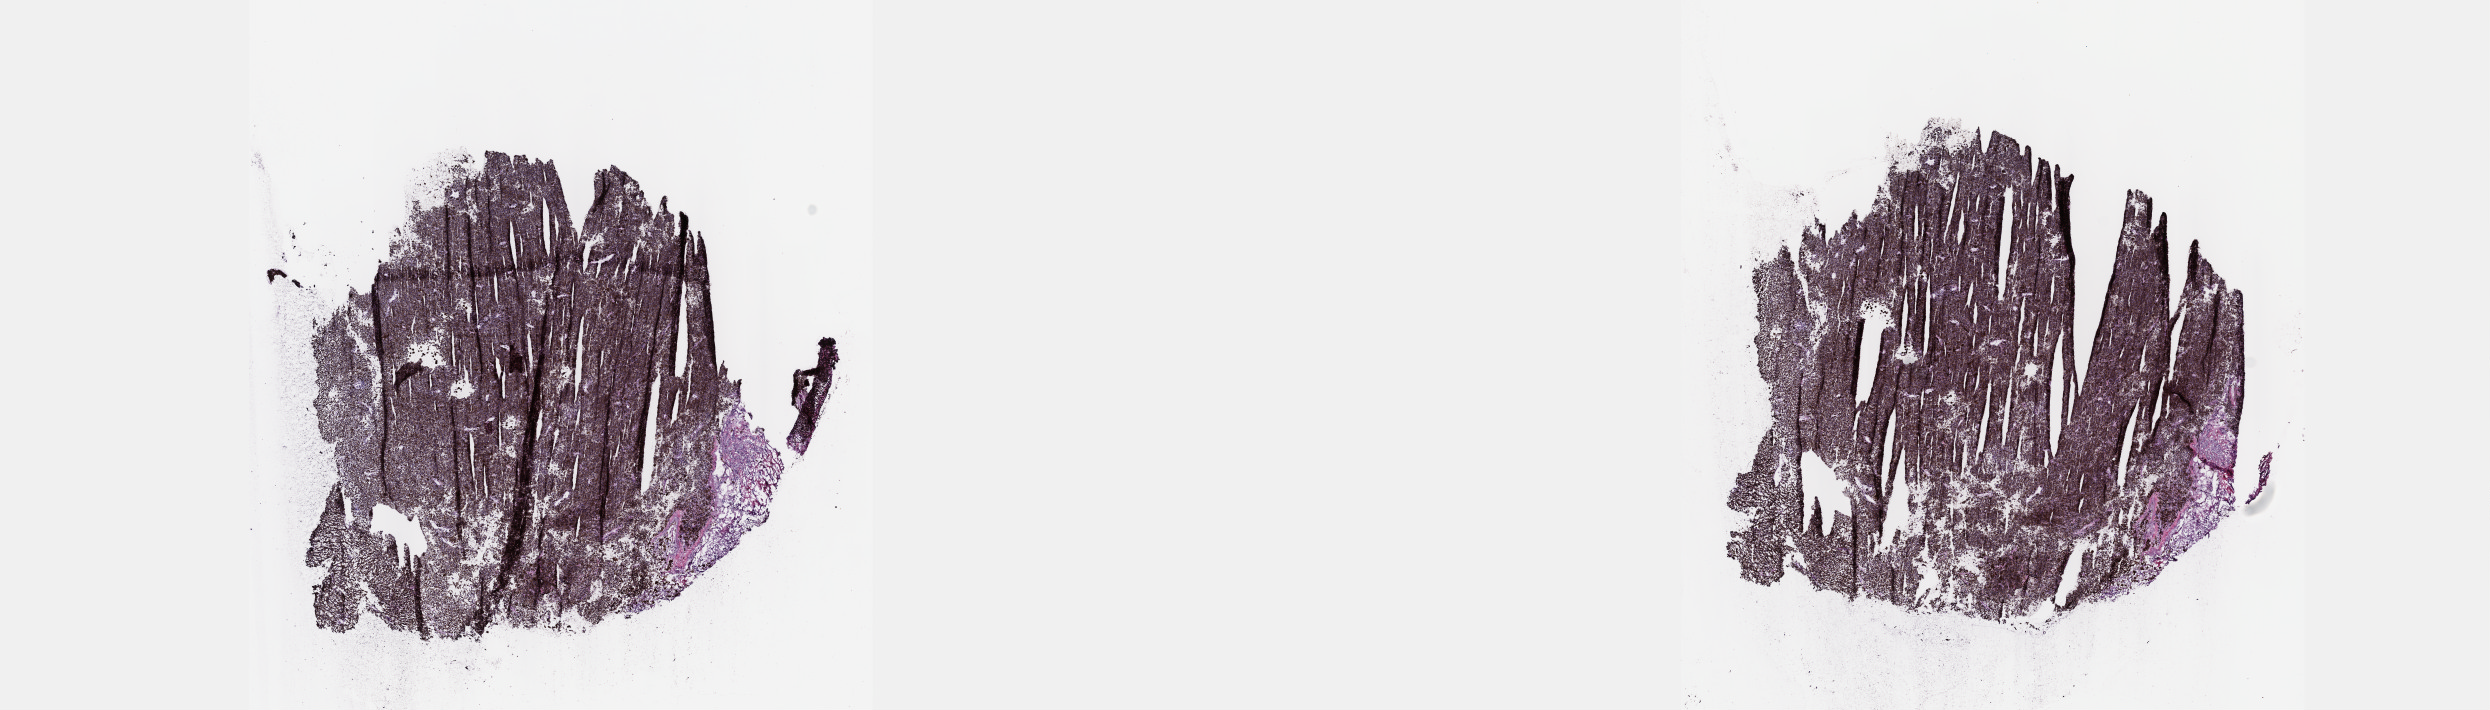
Digitized H&E-stained tissue section (whole slide) — low-resolution overview of the scanned area, about 20.1 x 5.7 mm (acquisition: 40x scan); frozen section from the top of the tissue portion; sample: primary tumour, uvea. Female, age 37 years at initial diagnosis. Pathologist review of this section (percent, as recorded): tumour cells 100%, tumour nuclei 80%, normal cells 0%, stromal cells 0%, necrosis 0%. Inflammatory infiltration, as recorded: lymphocyte infiltration 2%, monocyte infiltration 0%, neutrophil infiltration 0%.
AJCC pathologic stage: IIB (7th edition). Pathologic diagnosis: Spindle cell melanoma, NOS.